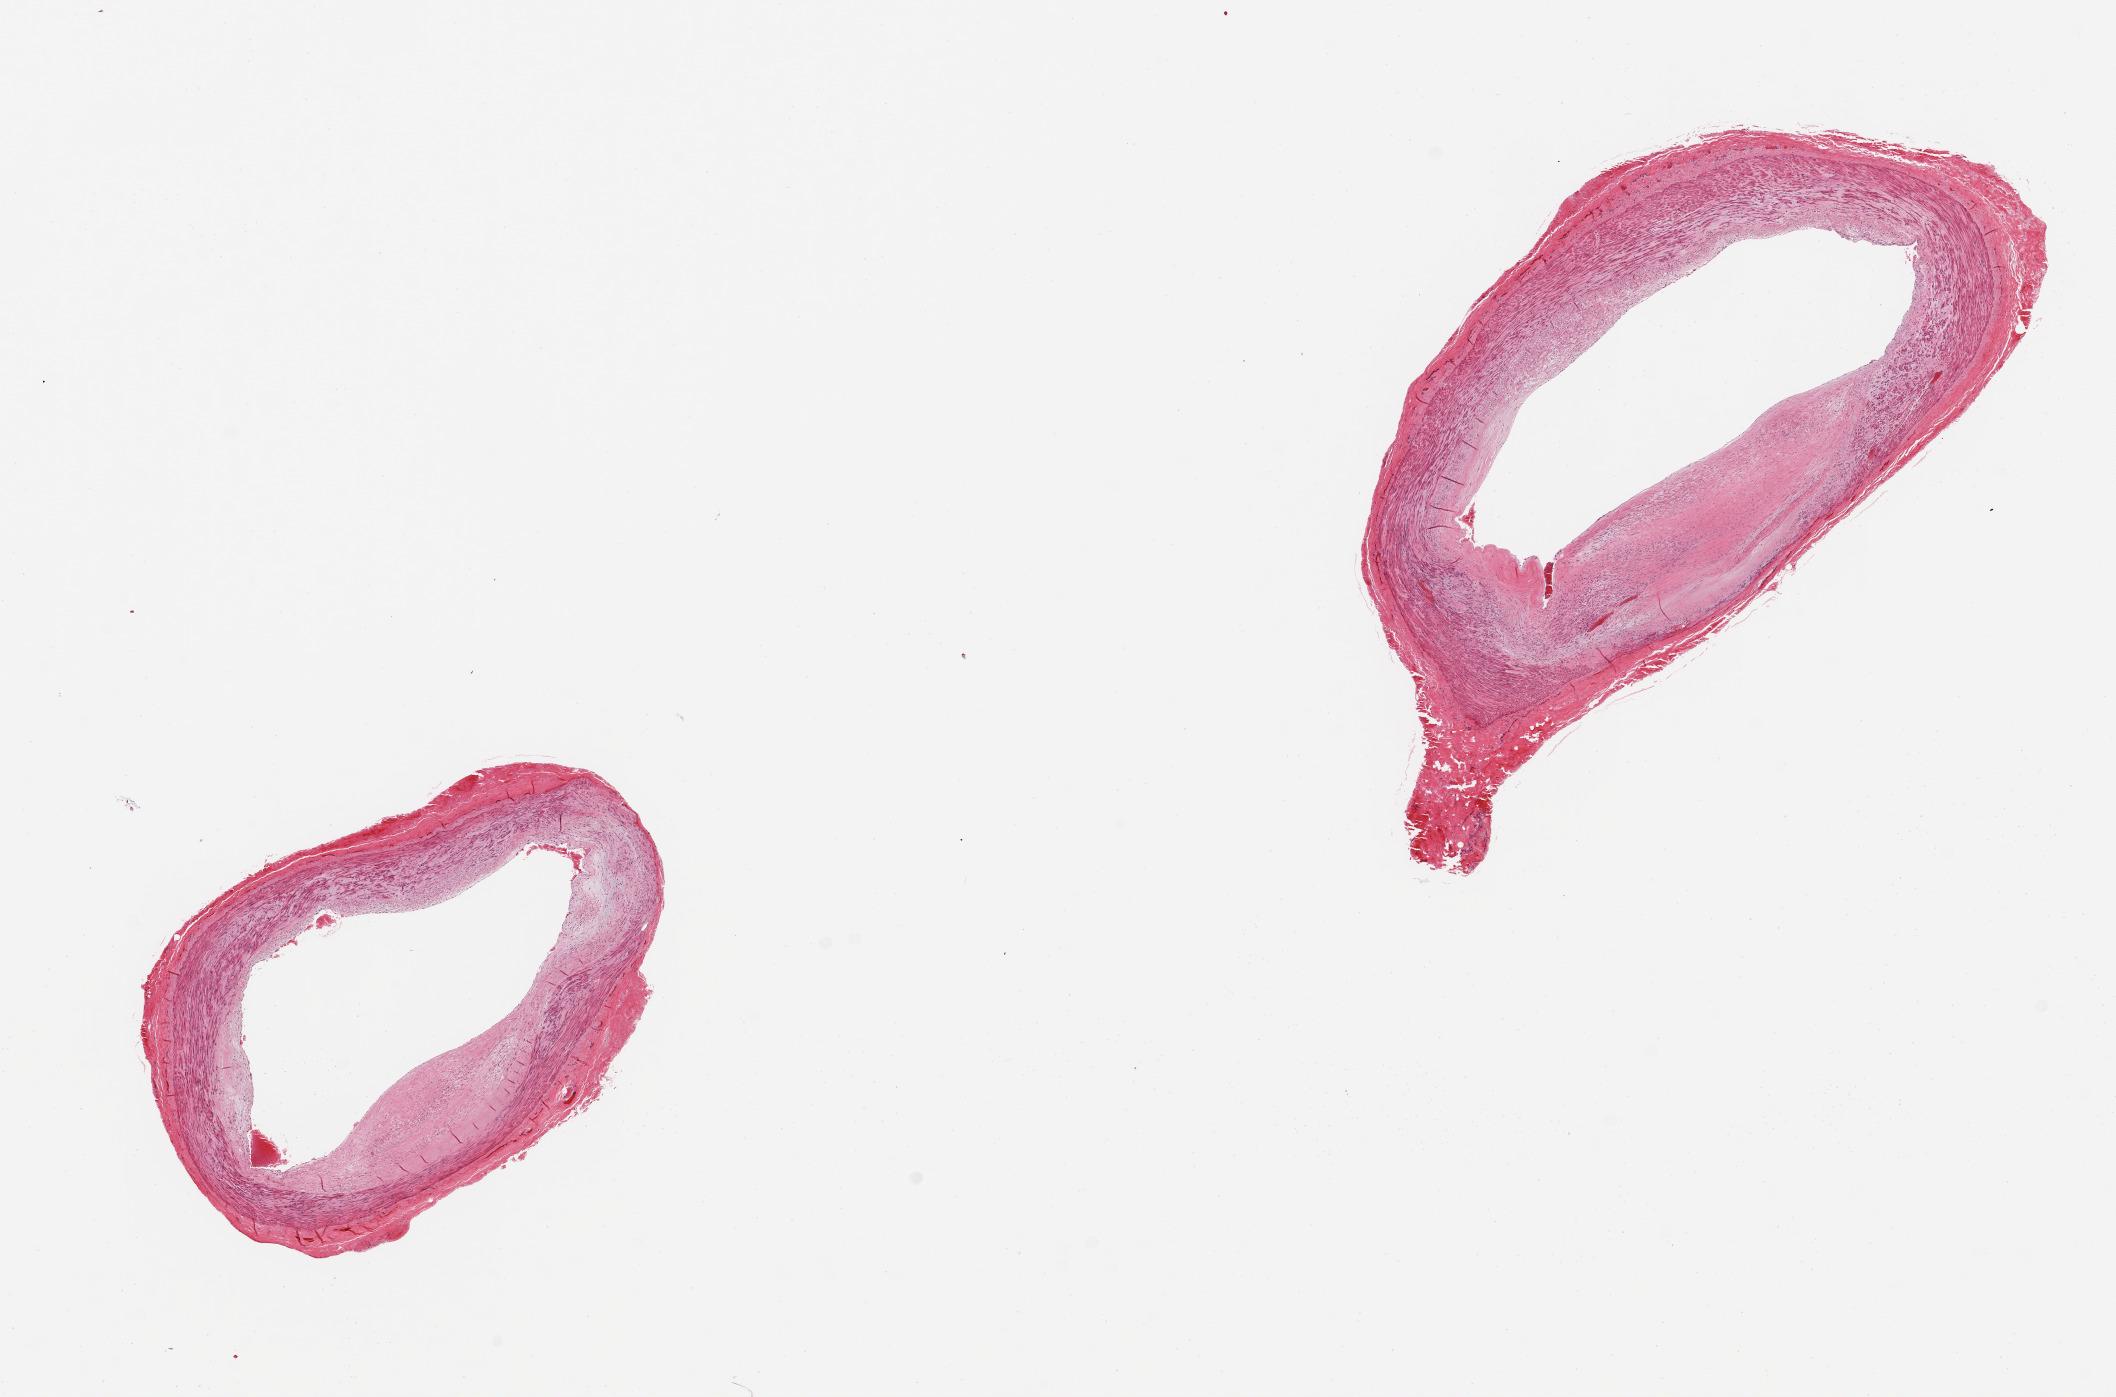
Digitized haematoxylin and eosin-stained section, shown as a low-resolution overview of the whole scanned area (about 16.7 x 11.0 mm, slide scanned at 20x); PAXgene-fixed, paraffin-embedded tissue; sampled site (target tissue): tibial artery; donor tissue sample. Donor: male.
- reviewer comment on this tissue sample: 2 pieces, atherosclerosis